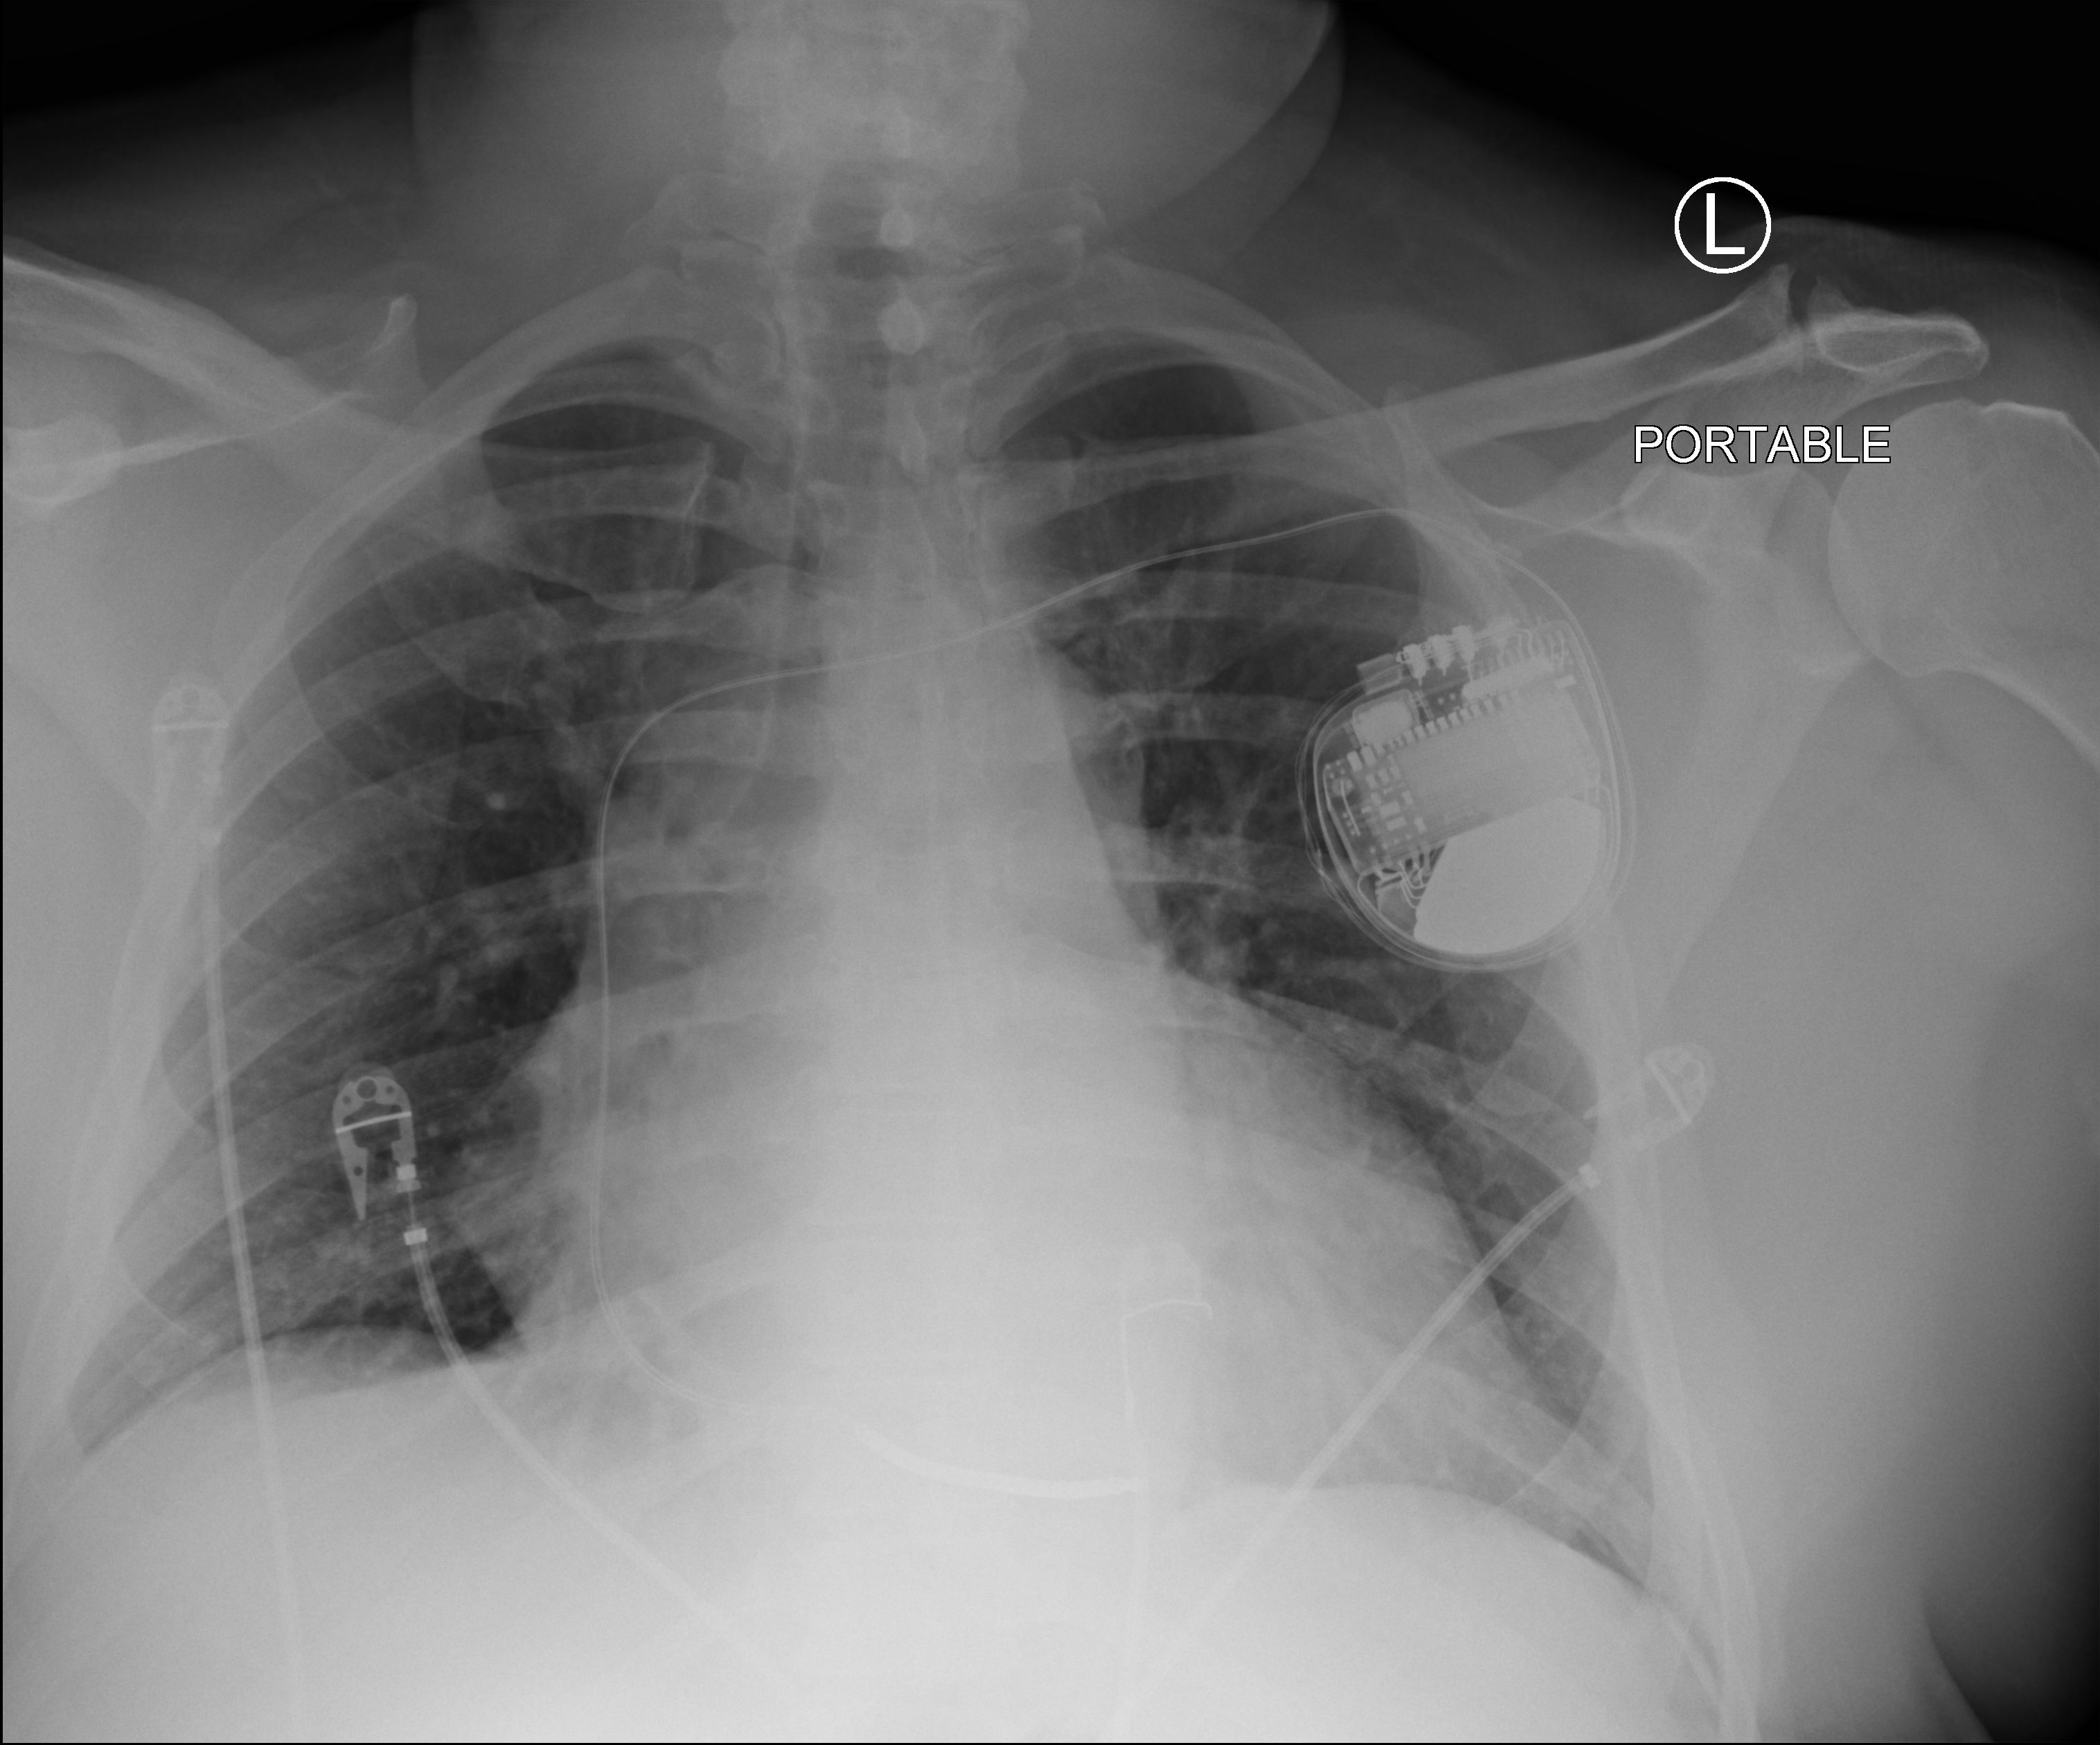
Portable chest radiograph. Patient hospitalised with COVID-19; male, aged 18–59 years.
Hospital-stay facts (about this admission, not read from this image; timing relative to this image not recorded):
- length of hospital stay: 4 days
- admitted to intensive care during this hospital stay: yes